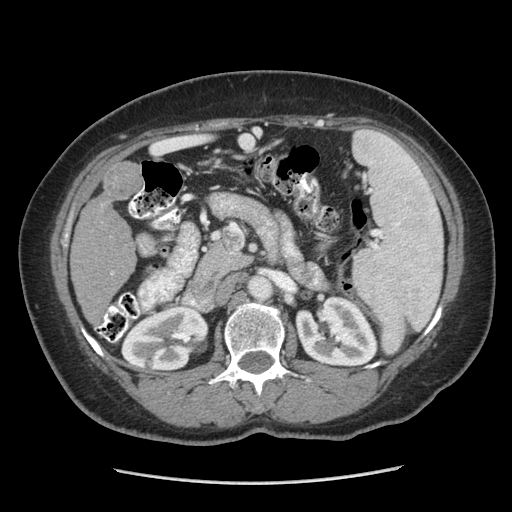
Contrast-enhanced abdominal CT (liver protocol), one axial slice. Slice 131 of 185 in the series (ordered by position). Soft-tissue window (W 400 / L 40 HU). 512 × 512 image matrix, field of view 360 × 360 mm. Case-level facts recorded for this patient, not image findings: diagnosis: hepatocellular carcinoma (patient treated with transarterial chemoembolisation; whether this scan precedes or follows treatment is not stated here); TNM stage (as recorded): Stage-I; Child-Pugh class: A; tumour differentiation: poorly differentiated.
Structures marked on this image (semi-automatic segmentation, software-assisted and operator-edited):
- liver parenchyma outside the tumour (the mass and vessels are separate outlines, so this box may not span the whole liver): bounding box <70,162,140,316> (left, top, right, bottom; pixels)
- mass: <105,164,140,199>